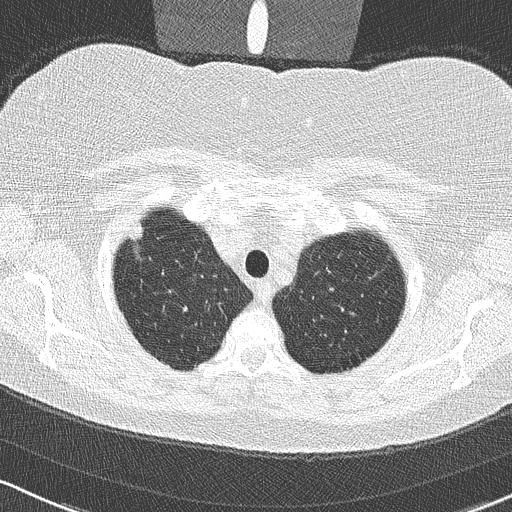
Low-dose screening chest CT, one axial slice. Slice 274 of 315 in the series (ordered by position). Reconstruction kernel B50f. 120 kVp. Lung window (W 1500 / L -600 HU). 2 mm slice thickness. 512 × 512 image matrix, field of view 320 × 320 mm.
Annotated regions visible in this slice (expert manual segmentation):
- lesion 1 (tumor, upper lobe of right lung): bounding box (x1, y1, x2, y2) in pixels: (129, 223, 143, 240)